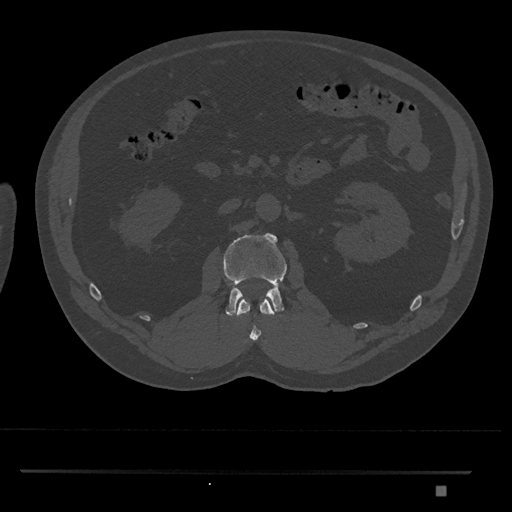
CT including the spine, one axial slice. Slice 780 of 1134 in the series (ordered by position). 120 kVp. Bone window (W 1800 / L 400 HU). 0.5 mm slice thickness. 512 × 512 image matrix. Male patient, age 65 years. Case-level facts recorded for this patient, not image findings: primary cancer: prostate.
Annotated regions visible in this slice (semi-automatically segmented with operator editing):
- L1 vertebra: bounding box <236,298,275,341> (left, top, right, bottom; pixels)
- L2 vertebra: <223,233,287,317>